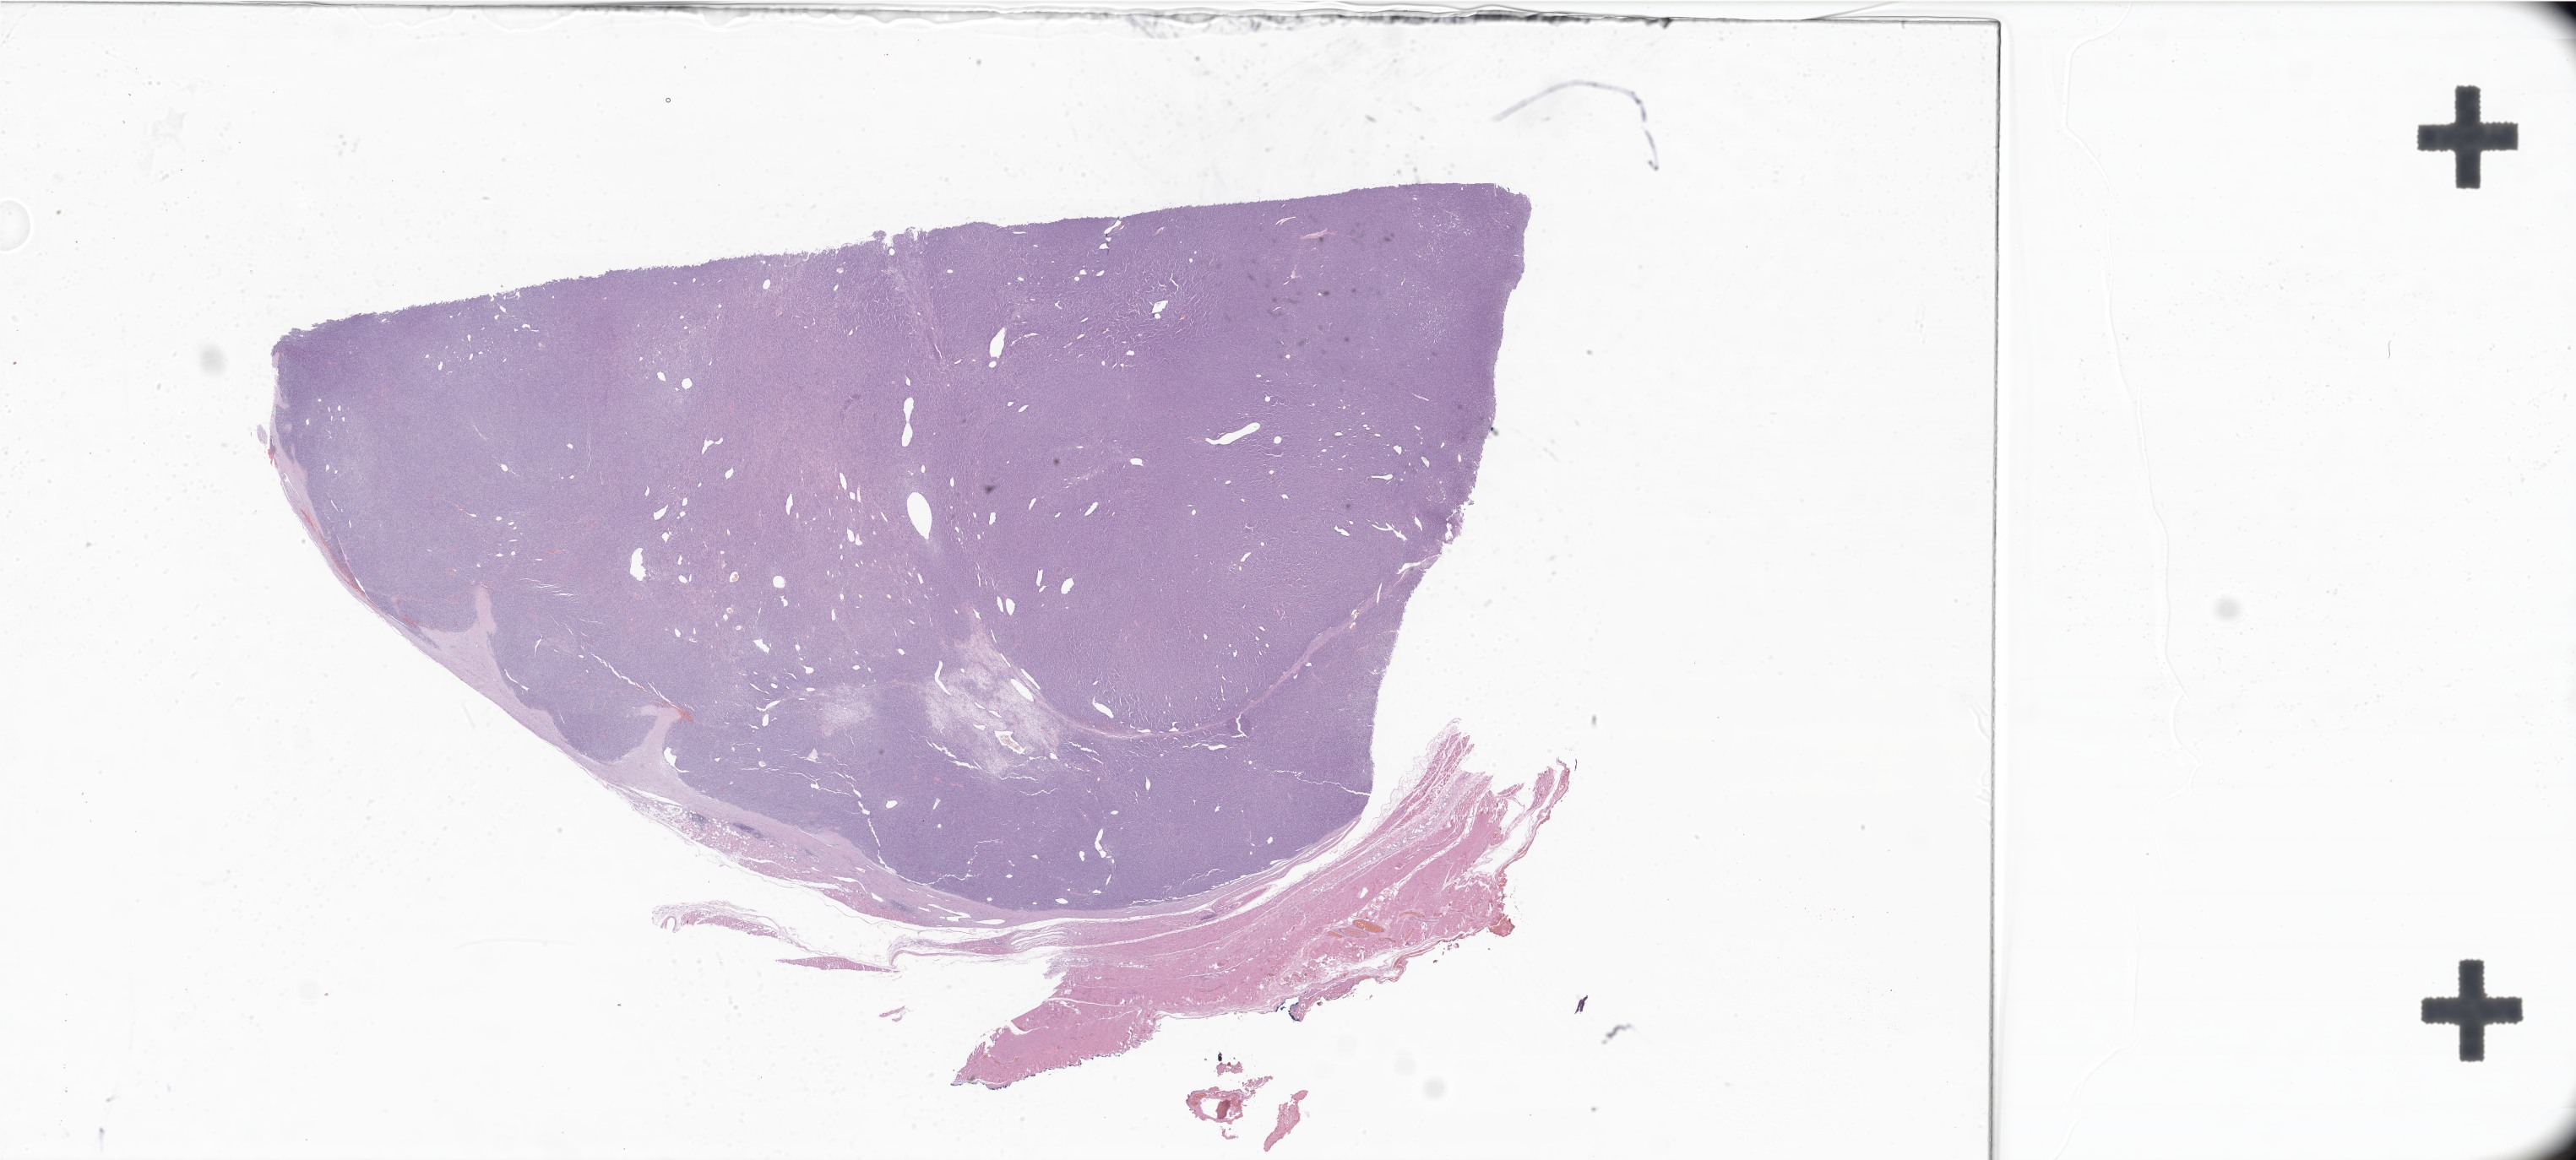
Digitized H&E-stained section of tumor tissue from the upper limb, shown as a low-resolution overview of the whole scanned area (about 51.4 x 23.2 mm). Formalin-fixed, paraffin-embedded (FFPE) tissue. Patient: female, age 161 months (13 years 5 months).
Diagnosis: Synovial sarcoma, spindle cell.